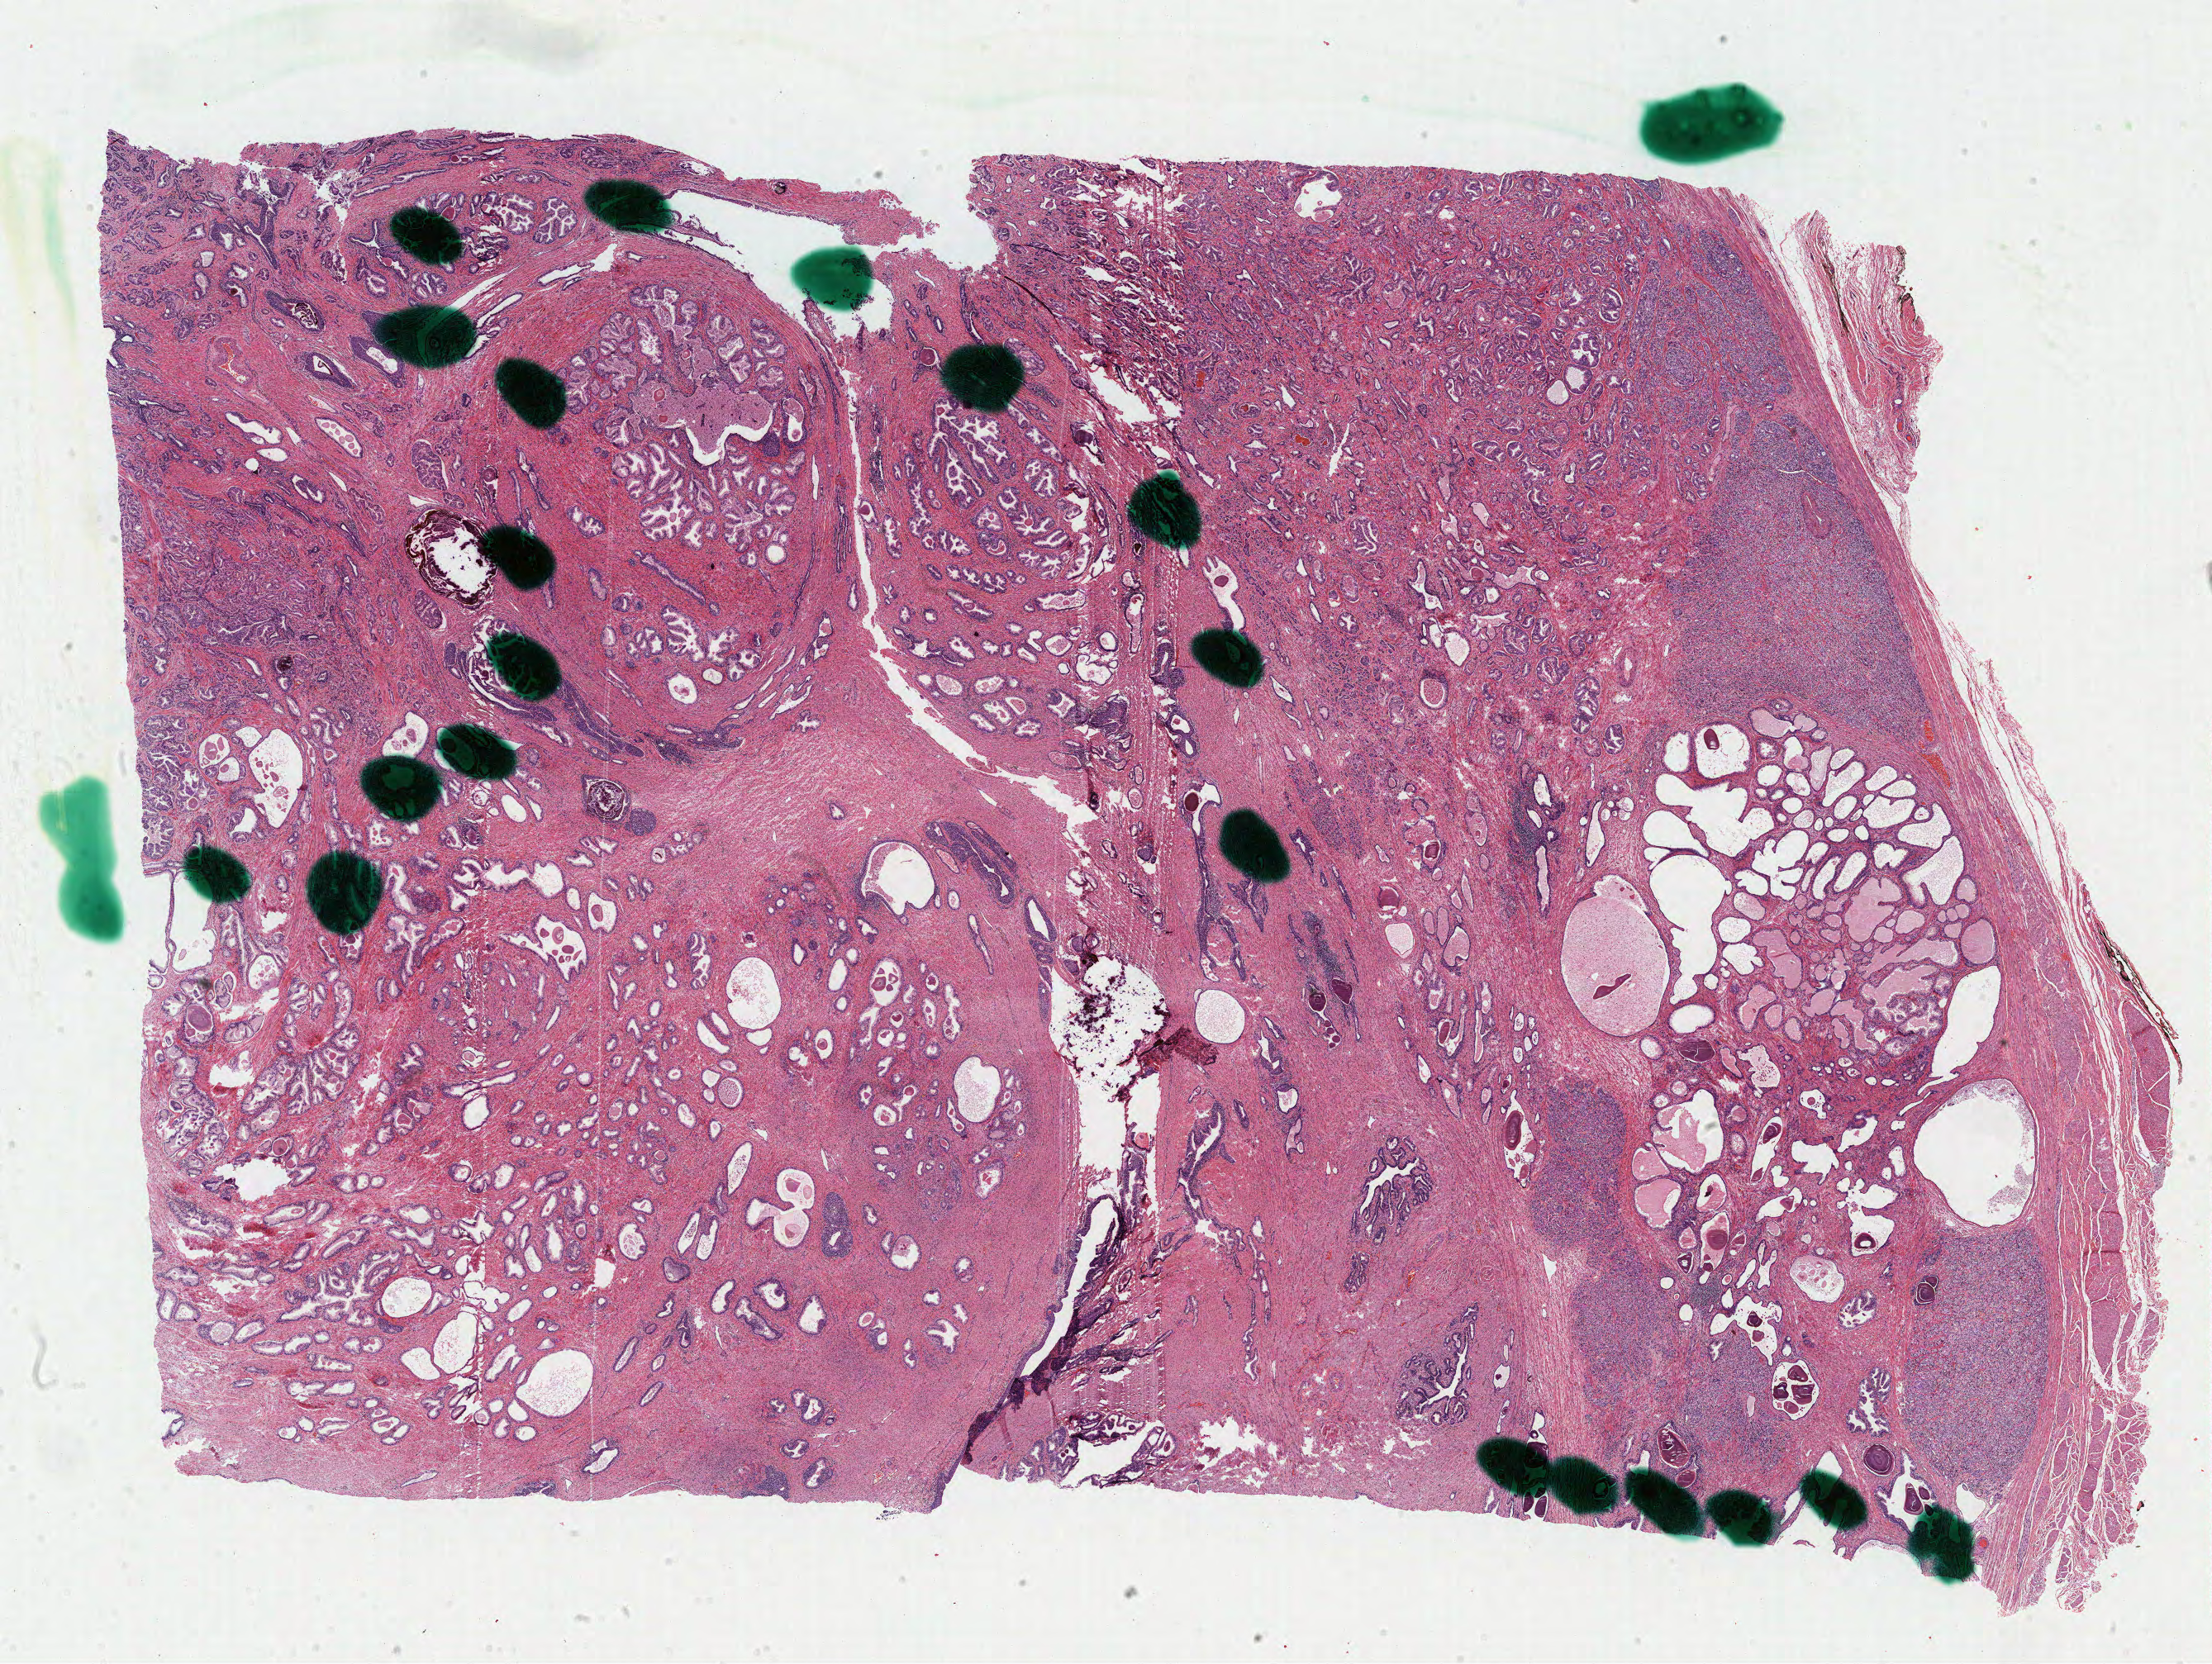
Whole-slide histology image, H&E-stained, shown as a low-resolution overview of the whole scanned area (about 21.2 x 16.0 mm), formalin-fixed paraffin-embedded (FFPE) diagnostic section, prostate, primary tumour sample. Patient: male, age at initial diagnosis 67 years. Gleason score: 9 (4+5).
Laterality: bilateral. Diagnosis: Adenocarcinoma, NOS (prostate gland). Lymph nodes positive (case pathology): 0 of 17 examined.